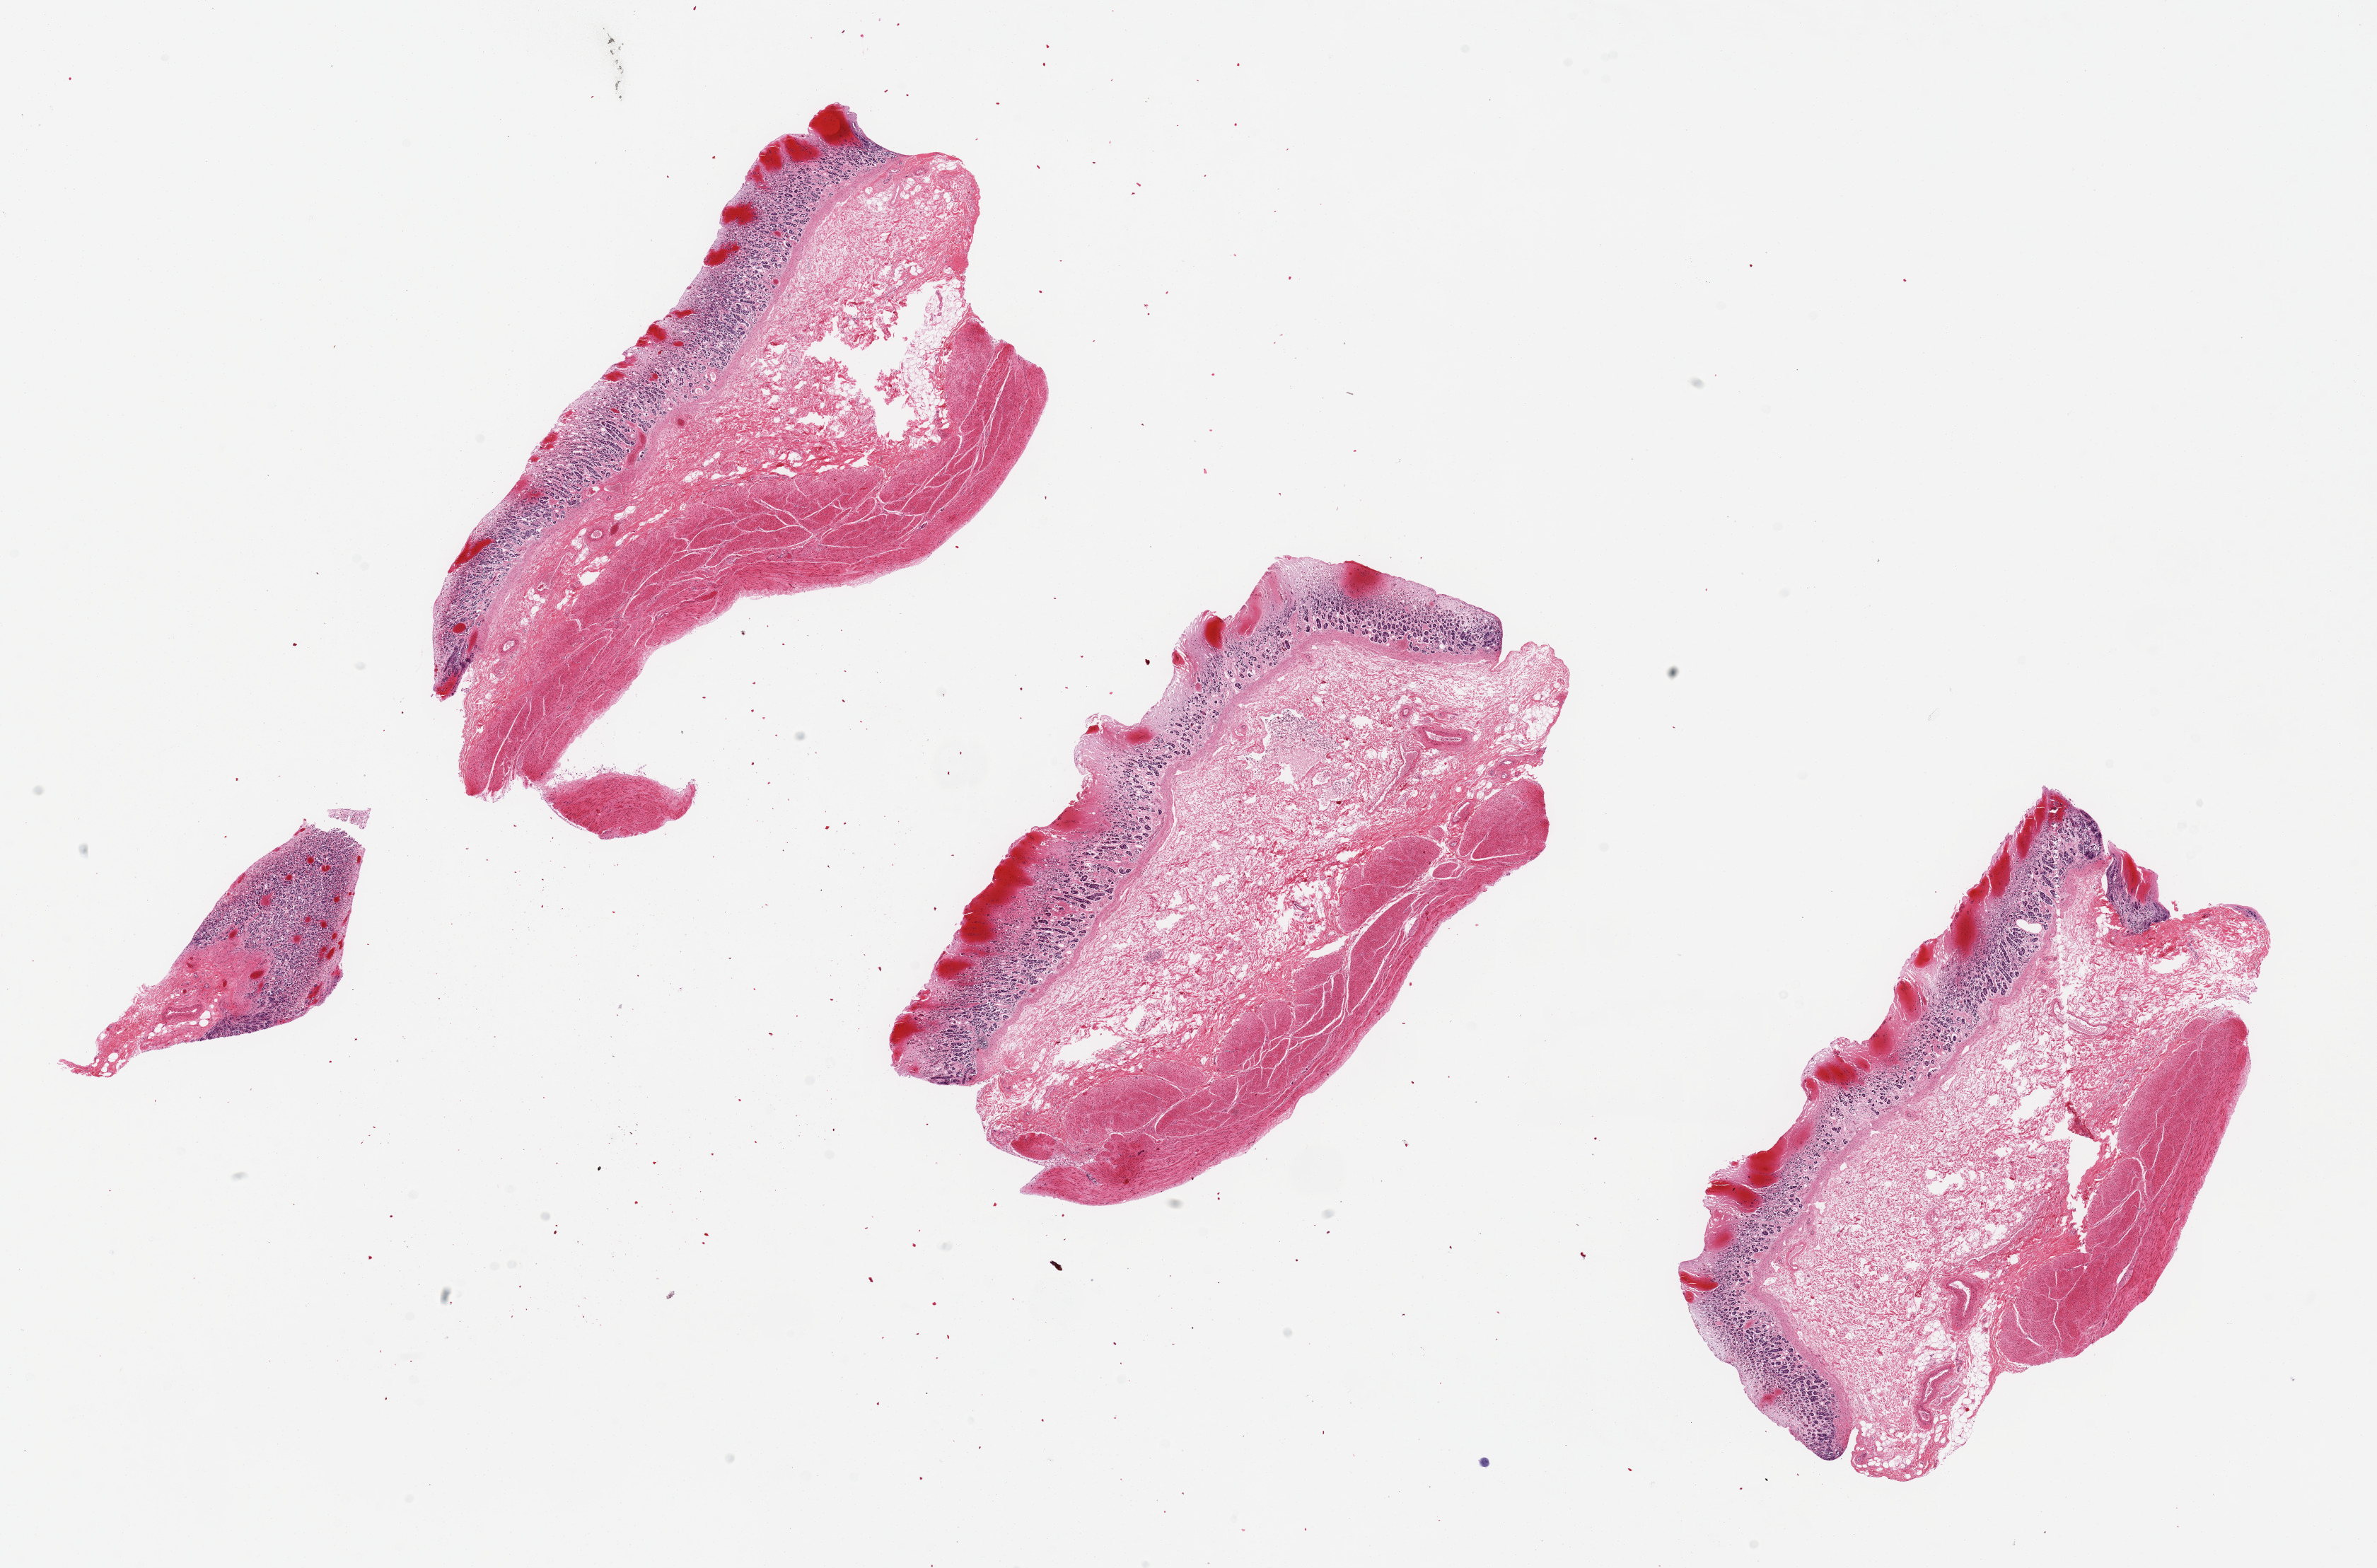
Digitized H&E-stained section, brightfield, a low-resolution overview of the entire scanned area, about 26.6 x 17.5 mm (acquisition: 20x scan); PAXgene-fixed, paraffin-embedded tissue; target tissue: stomach; tissue donor sample. Donor: male.
Review note (as recorded): Mucosa ~80% autolyzed.